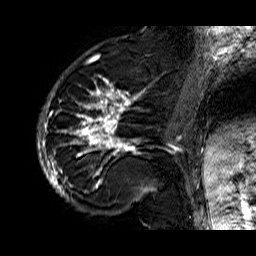
Breast MRI (dynamic contrast-enhanced), one sagittal slice; position 18 of 60 along the scan axis; dynamic contrast-enhanced series, time point 2 of 6 at this slice position (early post-contrast); 1.5 T; TE 6.3 ms, TR 32.9 ms; 256 × 256 image matrix. Female patient. From the clinical record (not read from this slice): setting: breast cancer imaged before/during neoadjuvant chemotherapy; receptor status: HR-positive, HER2-negative.
Annotated regions visible in this slice (semi-automatic segmentation, software-assisted and operator-edited):
- analysis volume of interest (the breast-tissue region the enhancement analysis was run in; not a lesion): bounding box (x1, y1, x2, y2) in pixels: (37, 74, 176, 210)
- tumour enhancement mask (voxels above the 100 % enhancement threshold inside the analysis volume of interest): (37, 77, 176, 205)